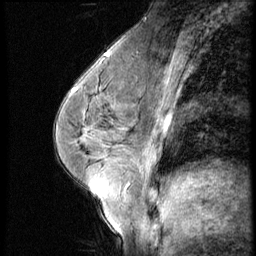
Breast MRI (dynamic contrast-enhanced), one sagittal slice. Slice 27 of 56 in the series (ordered by position). 3 images stored at this slice position (order not interpretable as contrast timing). 1.5 T. TE 4.2 ms, TR 9 ms. 256 × 256 image matrix. Female patient, age 45 years. Case-level facts recorded for this patient, not image findings: setting: breast cancer imaged before/during neoadjuvant chemotherapy; receptor status: HR-positive, HER2-negative.
Annotated regions visible in this slice (semi-automatic segmentation, software-assisted and operator-edited):
- analysis volume of interest (the breast-tissue region the enhancement analysis was run in; not a lesion): bounding box [x1, y1, x2, y2] px = [102, 77, 166, 129]
- tumour enhancement mask (voxels above the 140 % enhancement threshold inside the analysis volume of interest): [102, 80, 166, 127]